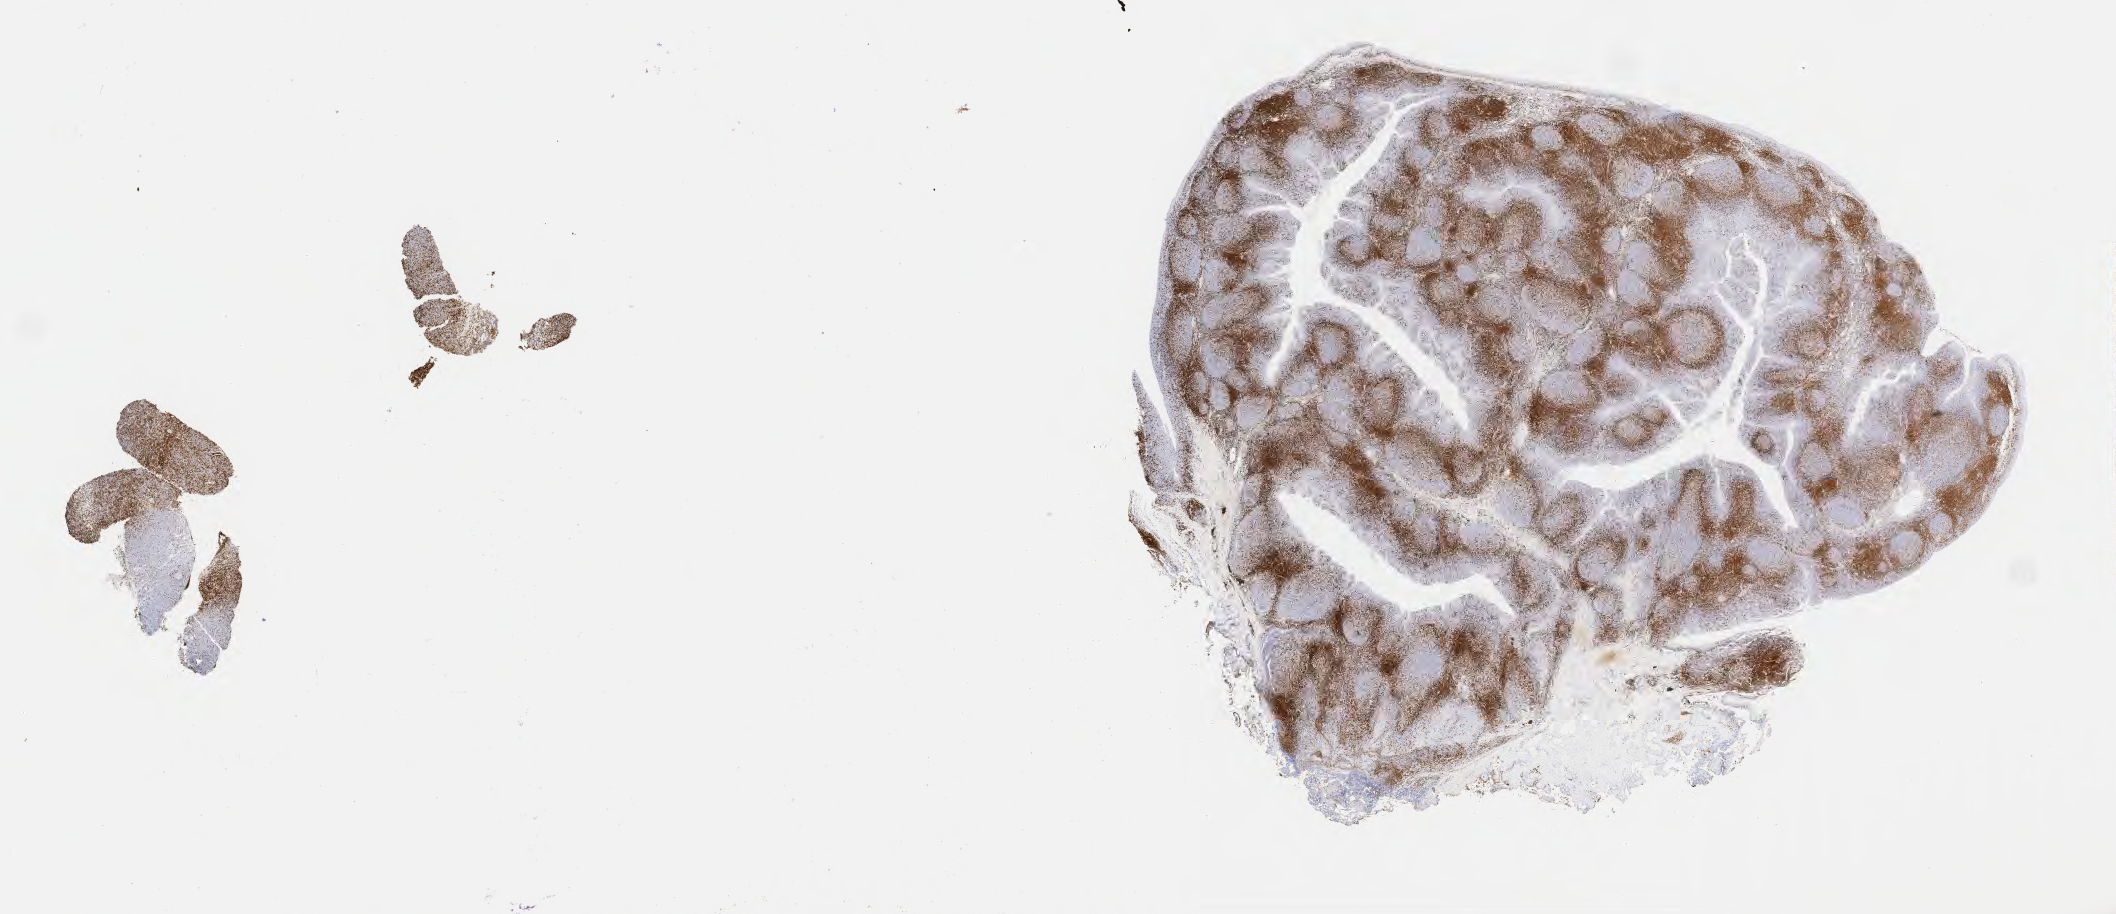
Immunohistochemistry (IHC) whole-slide image stained for CD3, a low-resolution overview of the entire scanned area, about 34.2 x 14.8 mm, tumor tissue, site: lymph node. Patient male; age 54 years.
• diagnosis: Diffuse large B-cell lymphoma, NOS